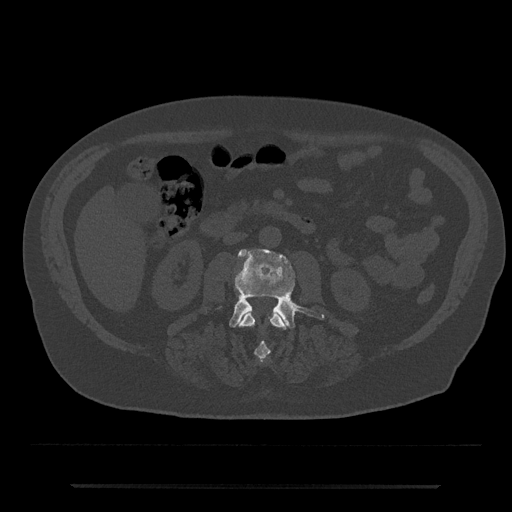
CT including the spine, one axial slice. Position 431 of 797 along the scan axis. Reconstruction kernel Br40s/3. 120 kVp. Bone window (W 1800 / L 400 HU). 512 × 512 image matrix, field of view 434 × 434 mm. Patient: male, 80 years. Case-level facts recorded for this patient, not image findings: primary cancer: prostate.
Structures marked on this image (semi-automatic segmentation, software-assisted and operator-edited):
- L2 vertebra: box from (x=240, y=310) to (x=286, y=361) px
- L3 vertebra: (x=207, y=249)–(x=324, y=328)